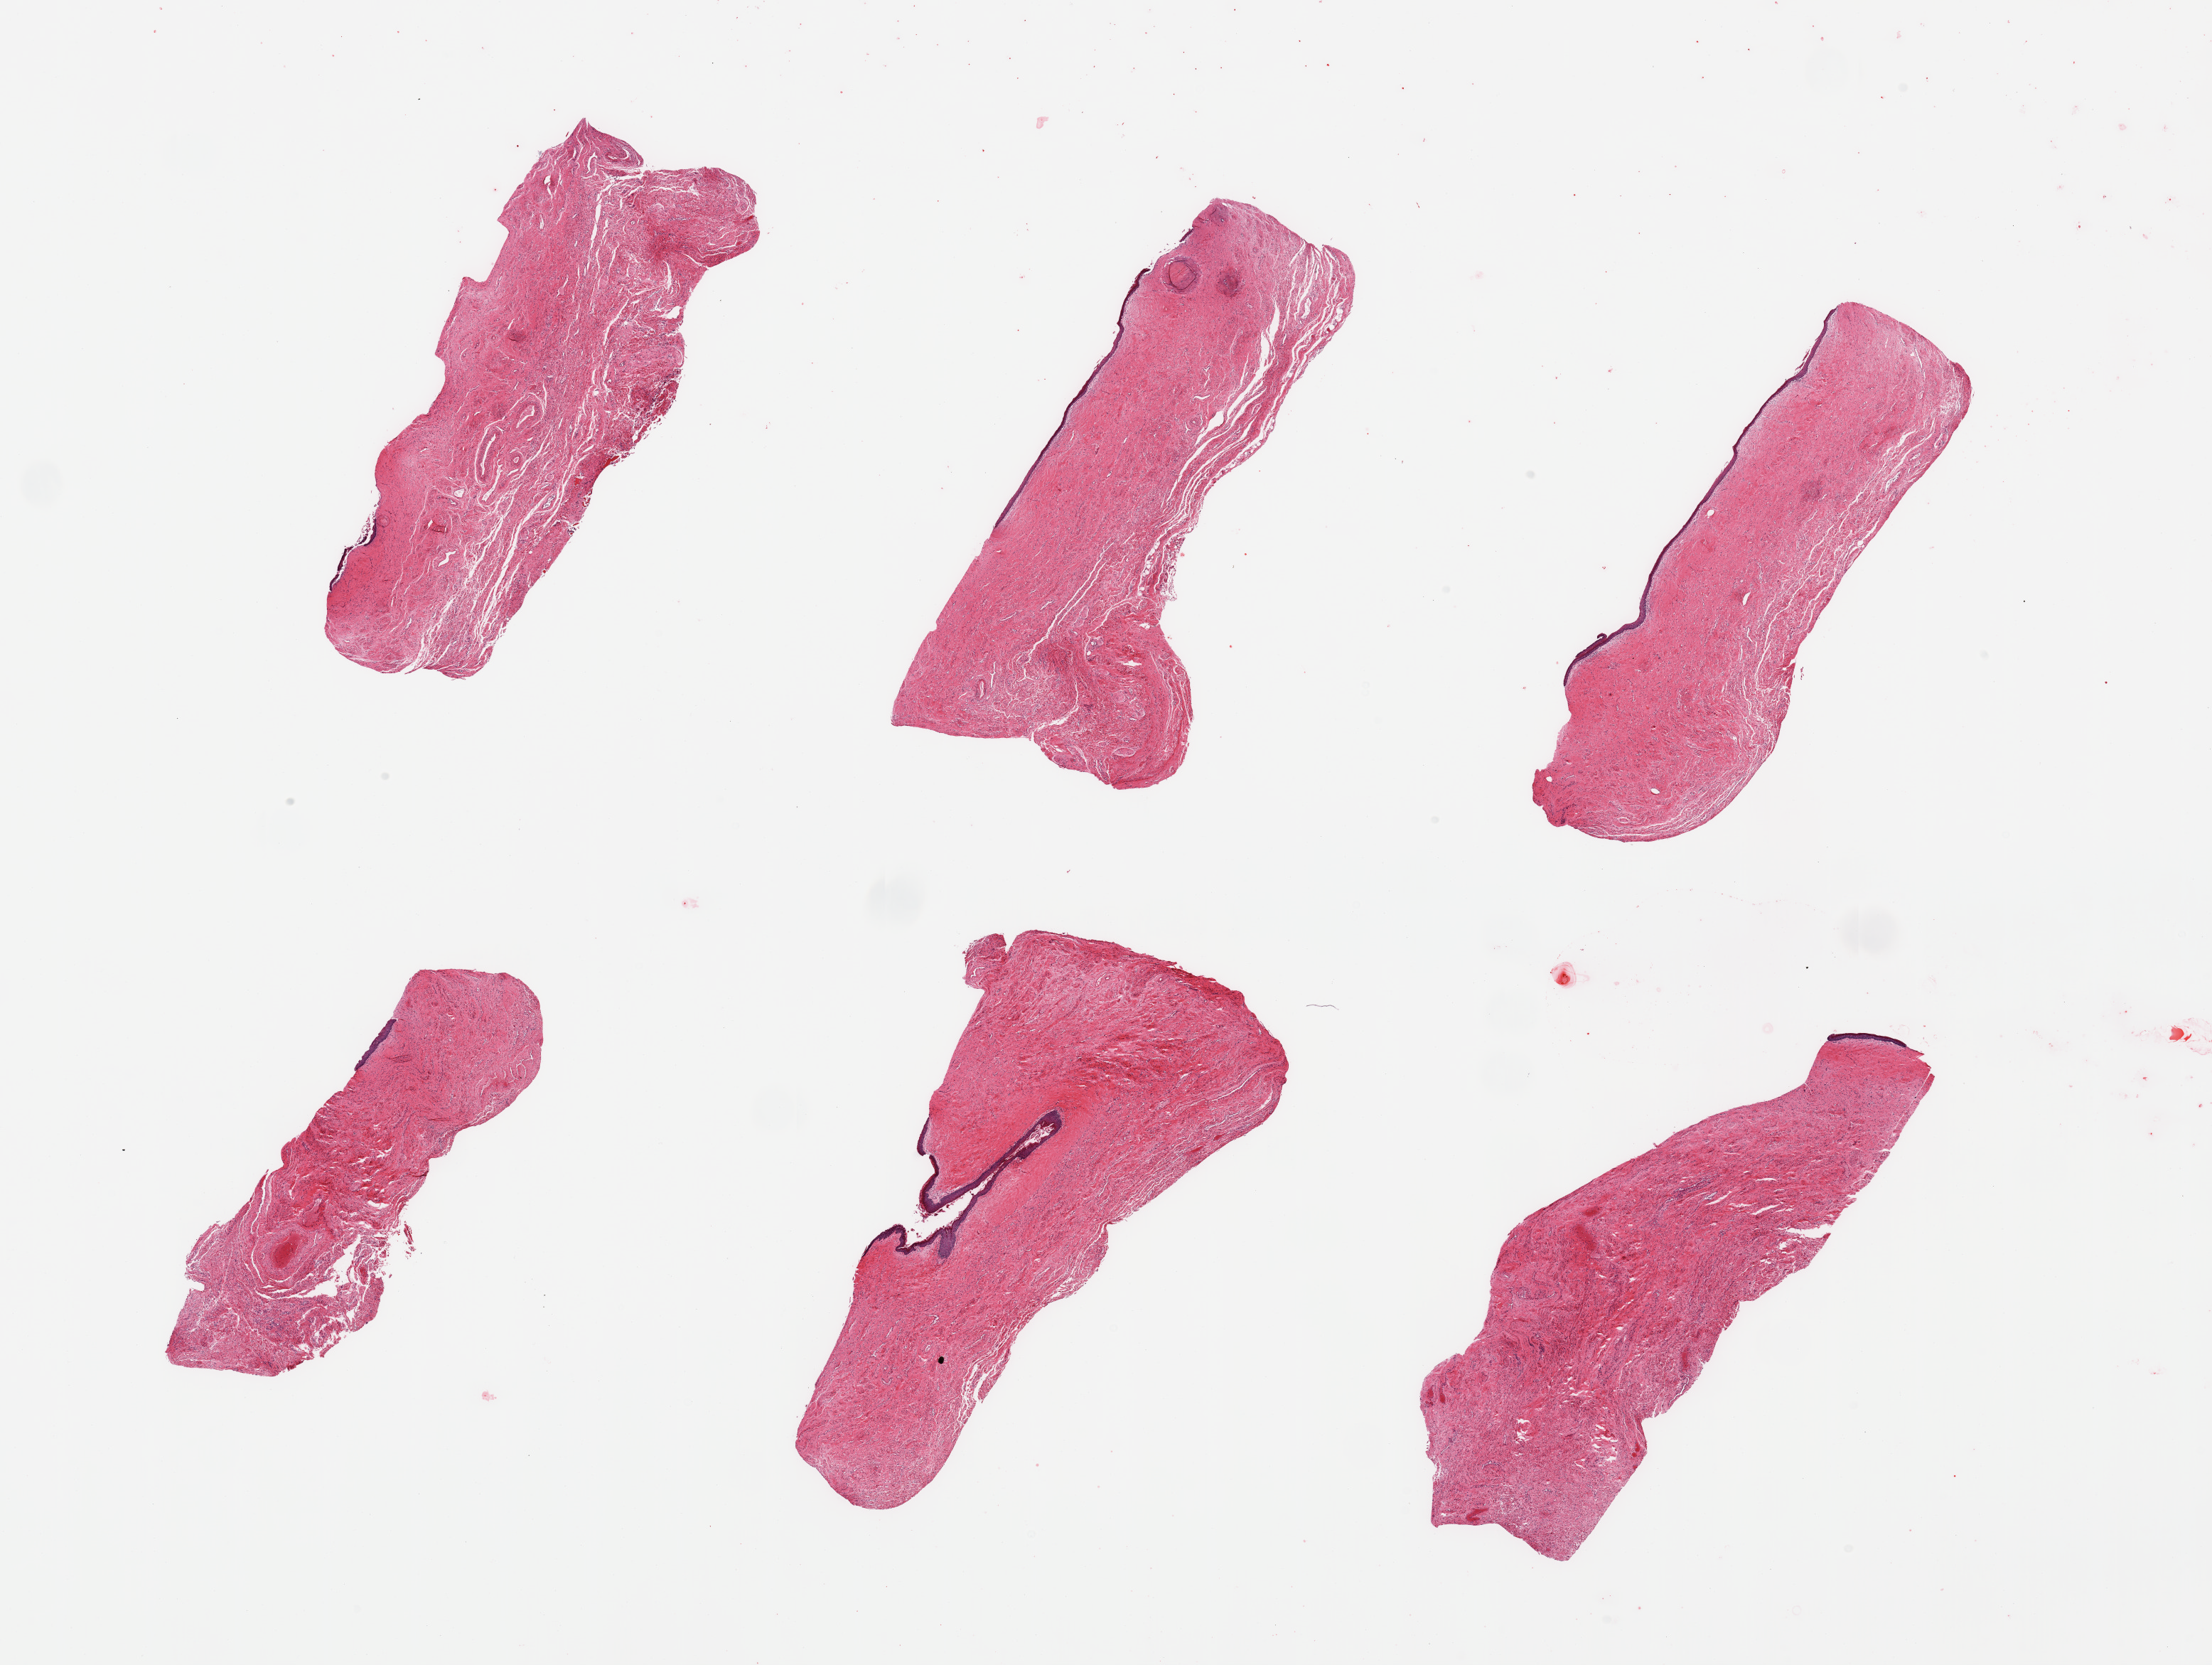
Haematoxylin and eosin whole-slide image — low-resolution overview of the scanned area, about 24.6 x 18.5 mm (acquisition: 20x scan), PAXgene-fixed paraffin-embedded (PFPE) section, section of vagina (target tissue), tissue donor sample. Female donor.
Review note (as recorded): 6 pieces; partially sloughed epithelium.